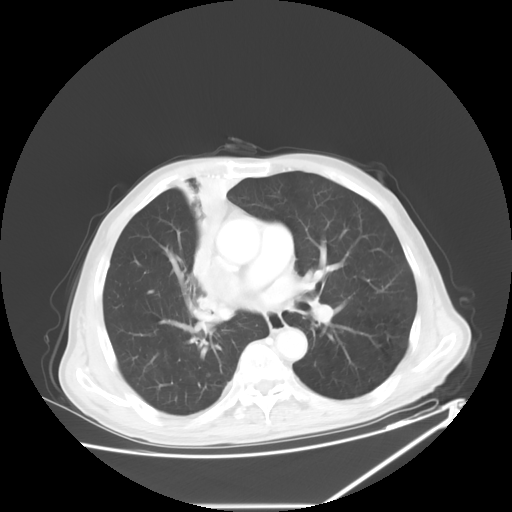
Chest CT, one axial slice. Position 34 of 60 along the scan axis. 120 kVp. Lung window (W 1500 / L -600 HU). 512 × 512 image matrix, field of view 410 × 410 mm. Patient: male, 73 years. From the clinical record (not read from this slice): clinical TNM (as recorded): T2a N1 M0.
Outlined on this slice (bounding box drawn by a radiologist):
- lung tumour (recorded histology: squamous cell carcinoma): bounding box <178,164,242,315> (left, top, right, bottom; pixels)